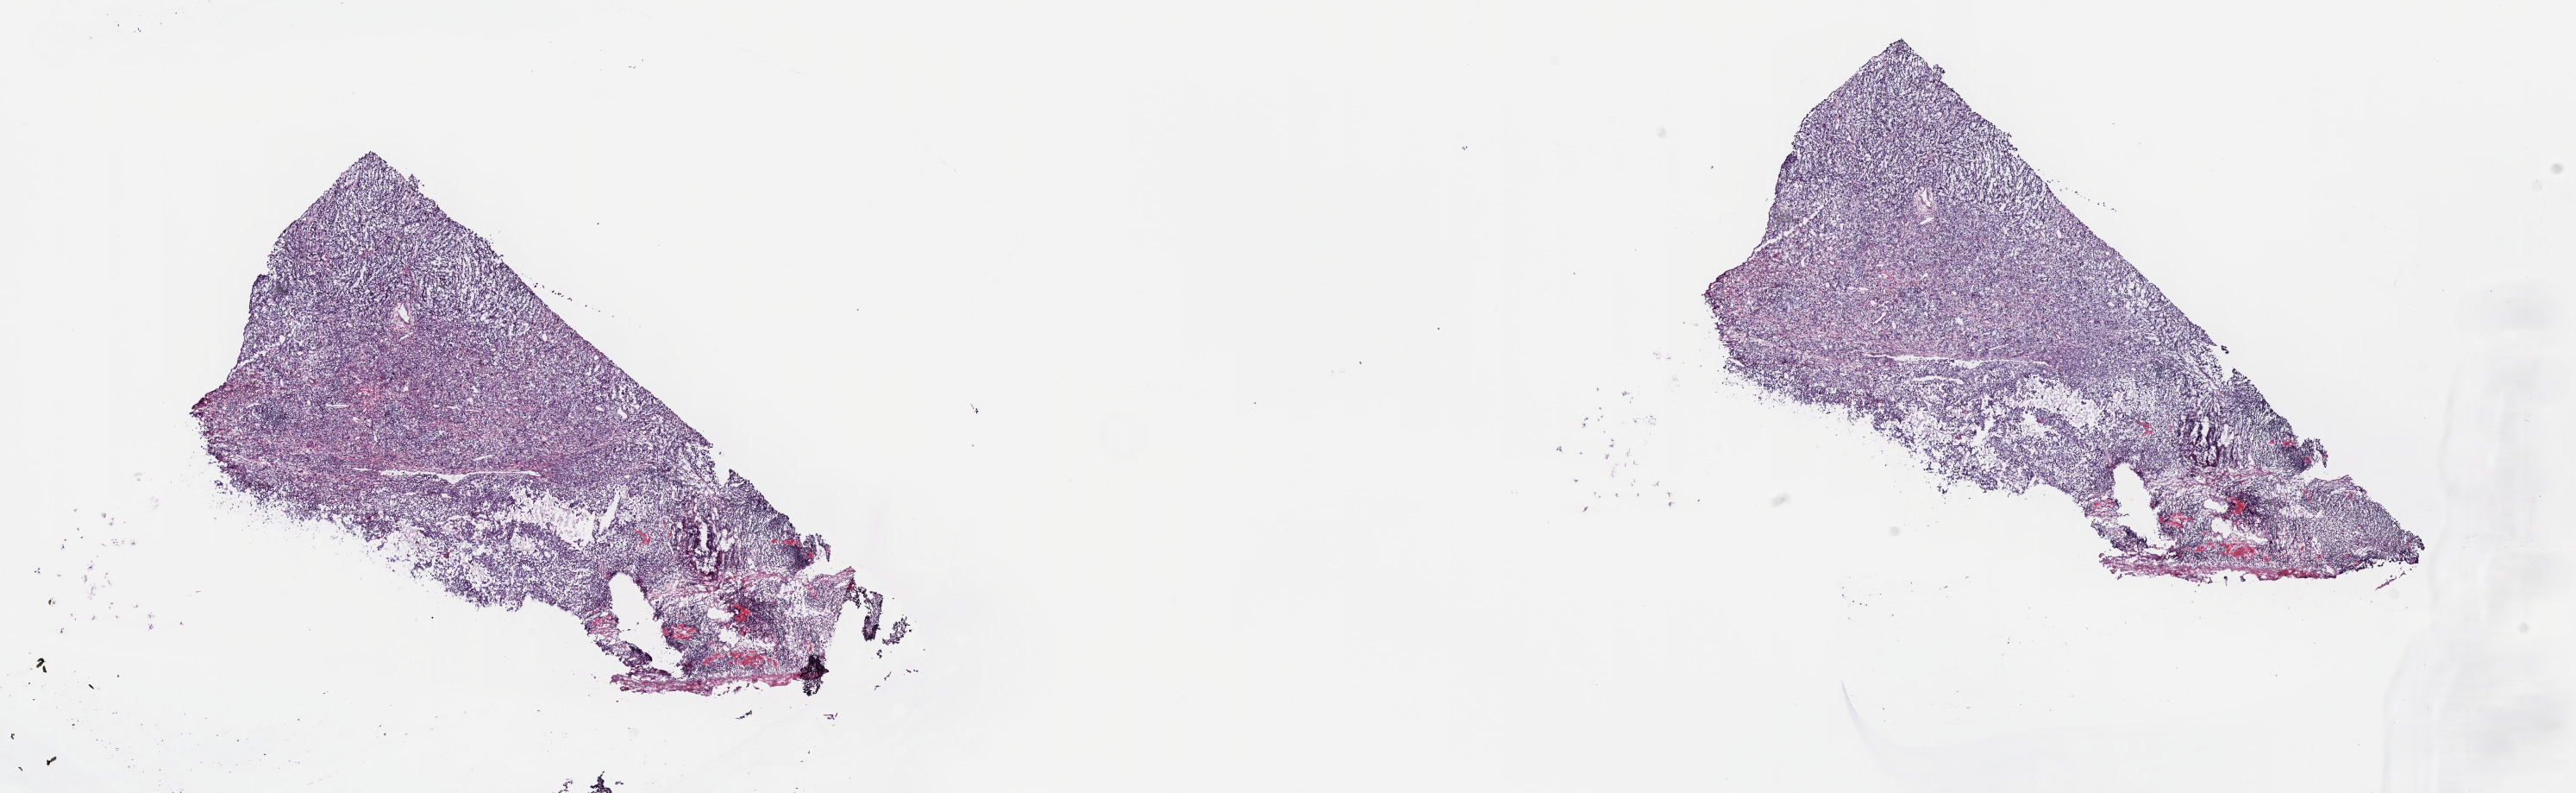
Whole-slide histology image, H&E, a low-resolution overview of the entire scanned area, about 24.2 x 7.4 mm; frozen section from the top of the tissue portion; metastatic tumour sample, sampled site not recorded. Female, age 59 years at initial diagnosis. Slide review estimates, as recorded: tumour cells 85%, tumour nuclei 85%, normal cells 0%, stromal cells 14%, necrosis 1%. Inflammatory infiltration, as recorded: lymphocyte infiltration 3%, monocyte infiltration 1%, neutrophil infiltration 2%.
- this section: metastatic tumour tissue
- patient diagnosis: Malignant melanoma, NOS